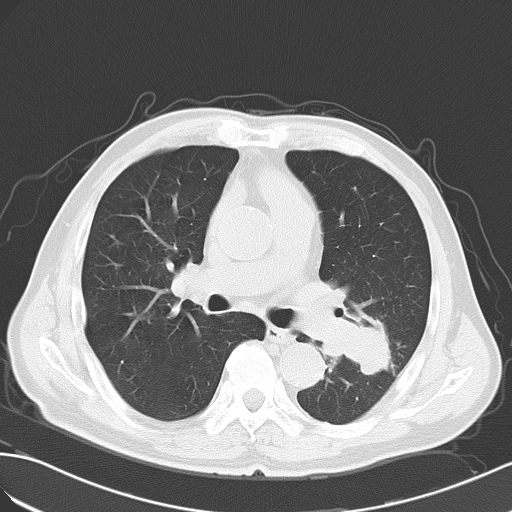
Chest CT, one axial slice; slice 32 of 55 in the series (ordered by position); reconstruction kernel B70f; 120 kVp; lung window (W 1500 / L -600 HU); 512 × 512 image matrix. Patient: male, 63 years. Case-level facts recorded for this patient, not image findings: clinical TNM (as recorded): T3 N3 M1a.
Outlined on this slice (bounding box drawn by a radiologist):
- lung tumour (recorded histology: large cell carcinoma): bounding box (x1, y1, x2, y2) in pixels: (315, 308, 389, 383)